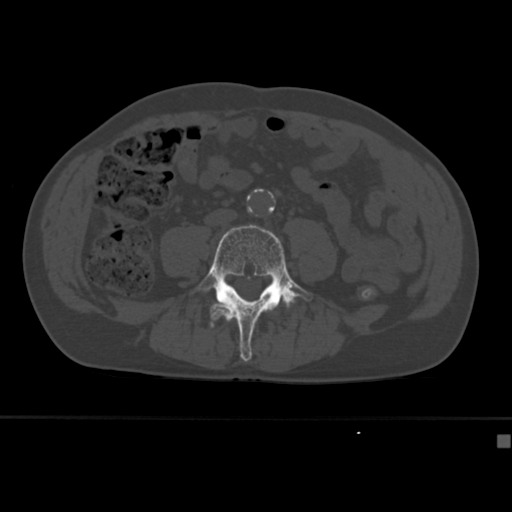
CT including the spine, one axial slice. Position 106 of 430 along the scan axis. 120 kVp. Bone window (W 1800 / L 400 HU). 1.5 mm slice thickness. 512 × 512 image matrix. Male patient, age 64 years. Case-level facts recorded for this patient, not image findings: primary cancer: uterus; vertebrae with lytic lesions (as recorded): T1, T4, T5, T7, L5.
Structures marked on this image (semi-automatically segmented with operator editing):
- L4 vertebra: bounding box (x1, y1, x2, y2) in pixels: (197, 224, 313, 362)